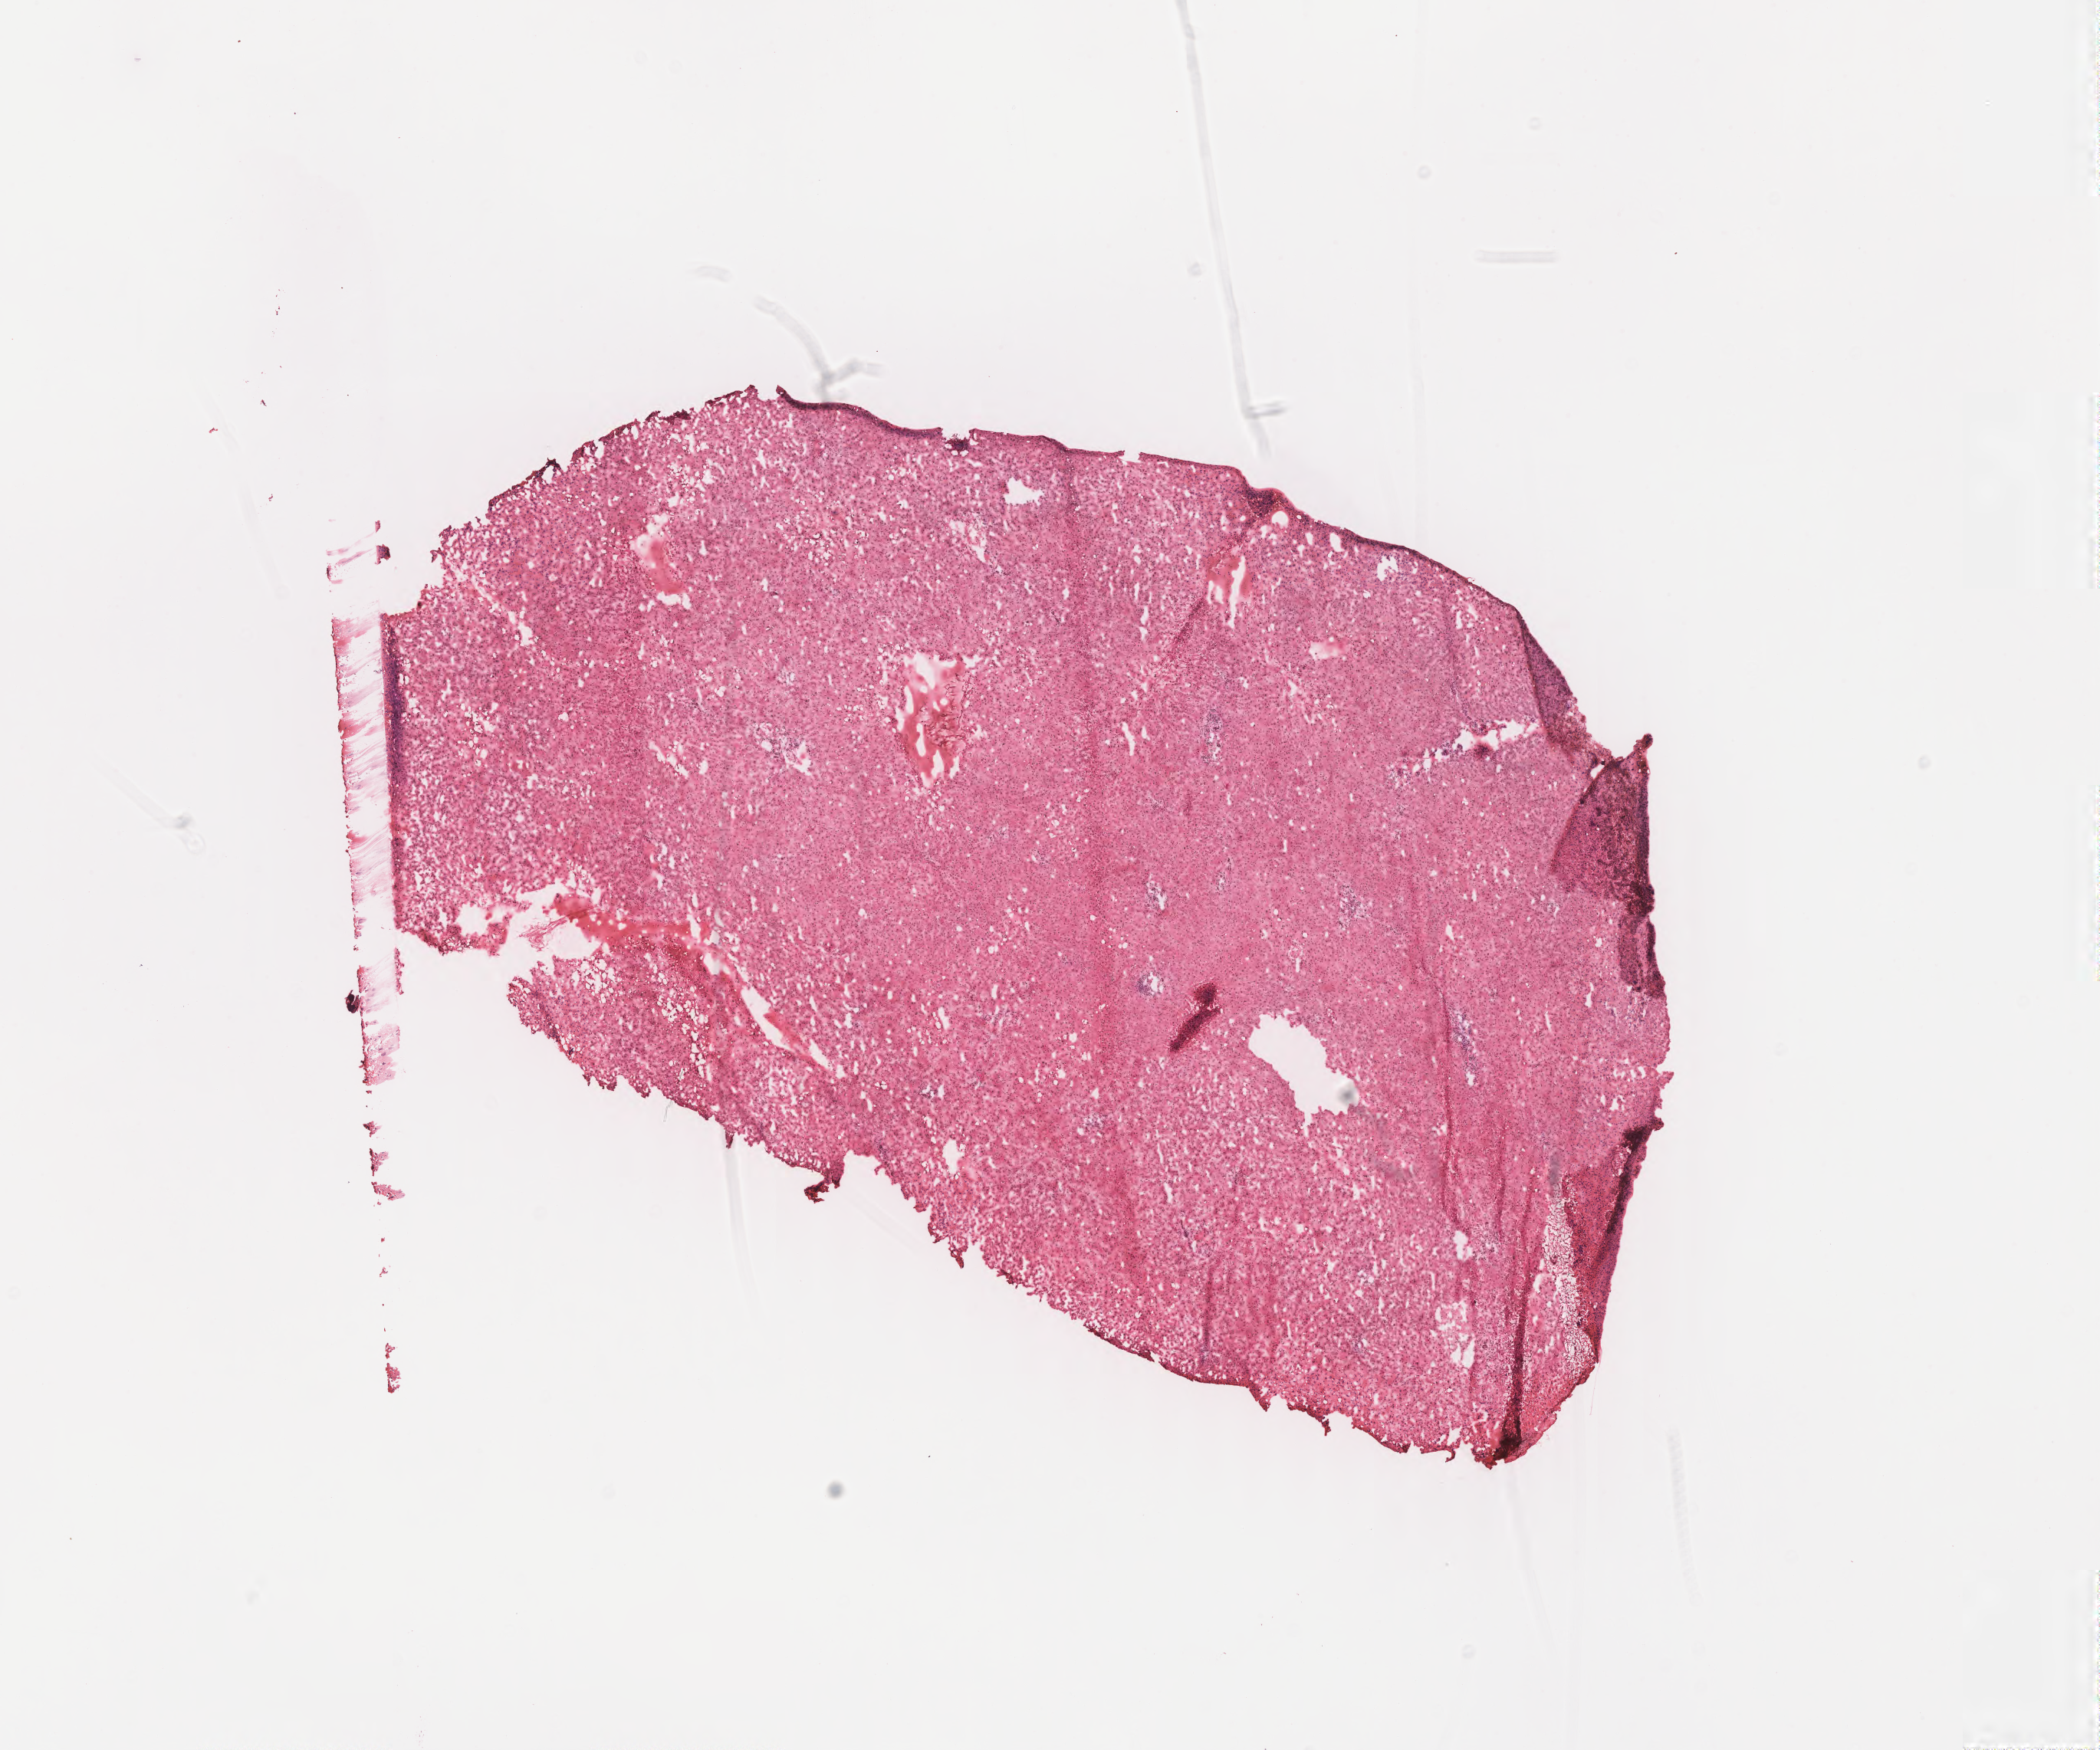
Whole-slide image, H&E stain — shown as a low-resolution overview of the whole scanned area (about 10.8 x 9.0 mm). Frozen section. Specimen: non-tumor (normal tissue) sample from a patient with adenocarcinoma, metastatic, NOS. Male, age 47 years at initial diagnosis. Composition of this section per pathologist review: tumor cells 0%, tumor nuclei 0%, stromal cells 10%, necrosis 0%, normal cells 90%. Infiltration values recorded for this section: lymphocyte infiltration 4%, monocyte infiltration 1%, neutrophil infiltration 2%.
• this section: non-tumor tissue sample; the patient's diagnosis is given above
• section: top of the tissue portion